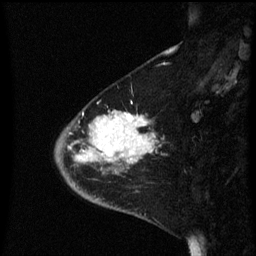
Breast MRI (dynamic contrast-enhanced), one sagittal slice. Slice 20 of 60 in the series (ordered by position). Dynamic contrast-enhanced series, image 2 of 3 at this slice position (ordered by acquisition). 1.5 T. TE 4.2 ms, TR 8.4 ms. 2.3 mm slice thickness. 256 × 256 image matrix, field of view 200 × 200 mm. Female patient, age 46 years. From the clinical record (not read from this slice): setting: breast cancer imaged before/during neoadjuvant chemotherapy; receptor status: HER2-positive.
Structures marked on this image (semi-automatically segmented with operator editing):
- analysis volume of interest (the breast-tissue region the enhancement analysis was run in; not a lesion): bounding box (x1, y1, x2, y2) in pixels: (55, 106, 159, 187)
- tumour enhancement mask (voxels above the 70 % enhancement threshold inside the analysis volume of interest): (69, 110, 154, 163)